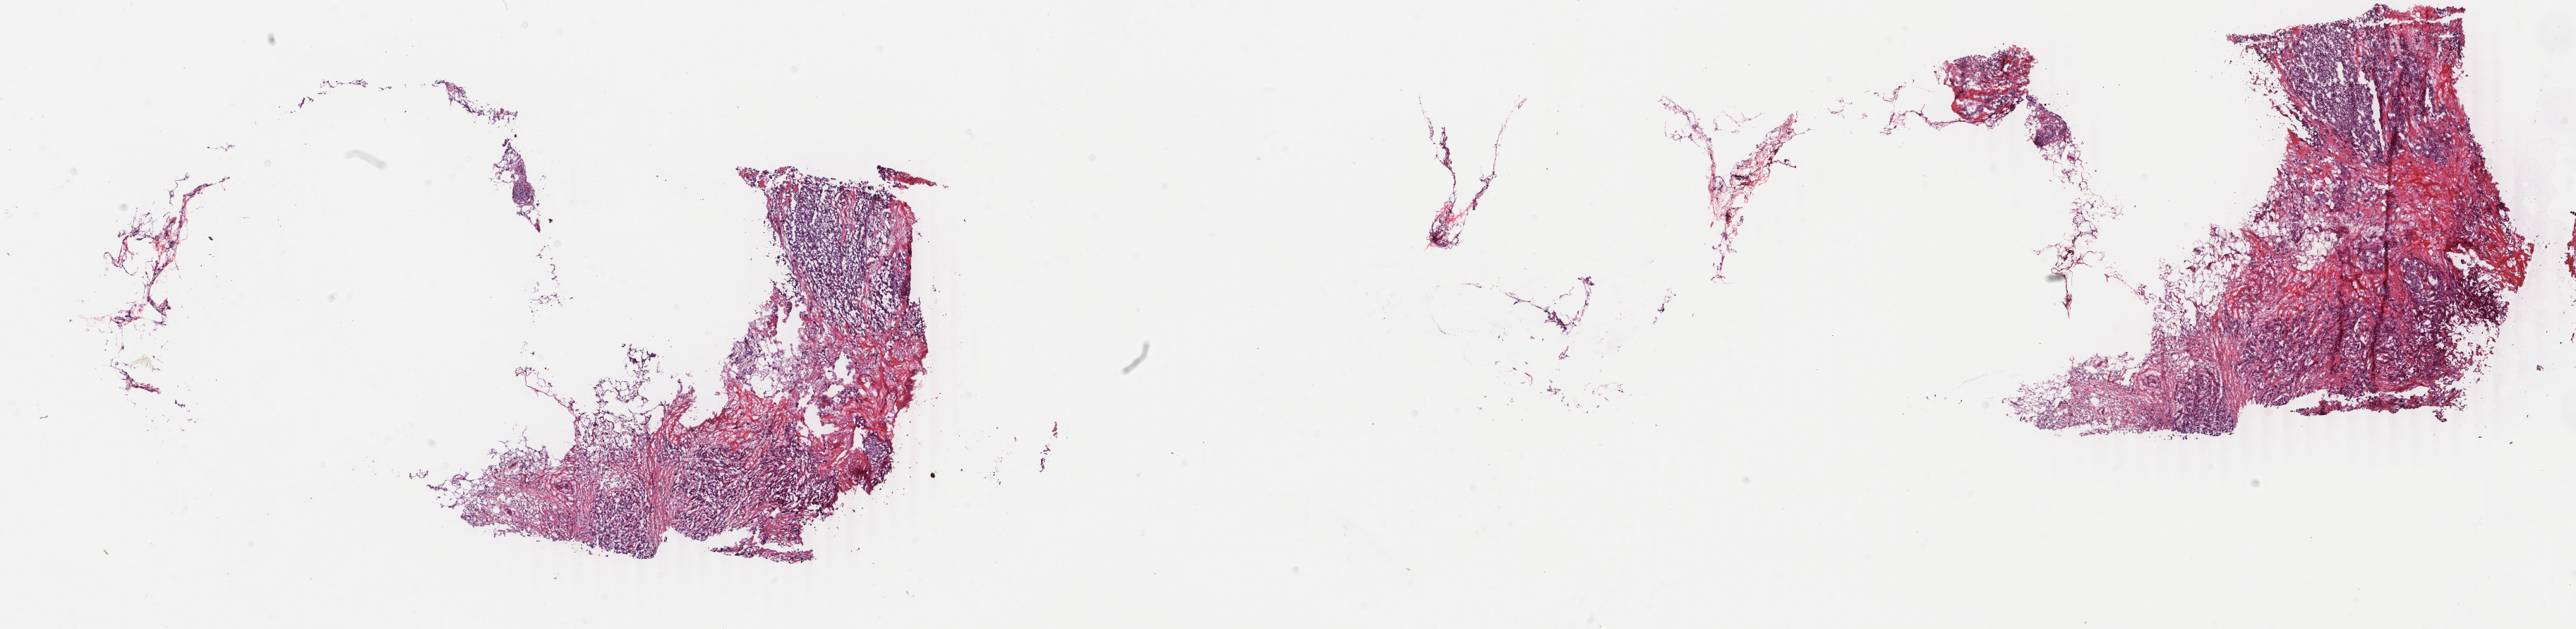
Hematoxylin and eosin (H&E) stained whole-slide image — shown as a low-resolution overview of the whole scanned area (about 29.0 x 7.1 mm). Frozen section from the top of the tissue portion. Primary tumour sample from the breast. Female patient; age at initial diagnosis 59 years. Pathologist review of this section (percent, as recorded): tumour cells 70%, tumour nuclei 70%, normal cells 0%, stromal cells 30%, necrosis 0%. Infiltration values recorded for this section: lymphocyte infiltration 4%, monocyte infiltration 1%, neutrophil infiltration 0%.
TNM: T2 N1mi M0. AJCC pathologic stage: IIB. Lymph nodes positive (case pathology): 1 of 3 examined. Diagnosis: Infiltrating duct carcinoma, NOS.